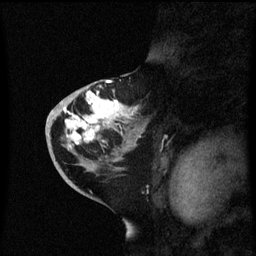
Breast MRI (dynamic contrast-enhanced), one sagittal slice; position 33 of 60 along the scan axis; dynamic contrast-enhanced series, image 2 of 3 at this slice position (ordered by acquisition); 1.5 T; TE 4.2 ms, TR 8.4 ms; 2.3 mm slice thickness; 256 × 256 image matrix. Patient: female, 46 years. Case-level facts recorded for this patient, not image findings: setting: breast cancer imaged before/during neoadjuvant chemotherapy; receptor status: HER2-positive.
Structures marked on this image (semi-automatically segmented with operator editing):
- analysis volume of interest (the breast-tissue region the enhancement analysis was run in; not a lesion): box from (x=46, y=86) to (x=147, y=171) px
- tumour enhancement mask (voxels above the 70 % enhancement threshold inside the analysis volume of interest): (x=64, y=90)–(x=131, y=149)